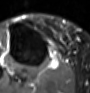
MRI of an extremity soft-tissue mass, one axial slice; slice 43 of 60 in the series (ordered by position); STIR; MR volume resampled by the dataset authors to the PET/CT grid (not the native acquisition matrix); 3.27 mm slice thickness; 90 × 93 image matrix, field of view 88 × 91 mm. Female patient. Case-level facts recorded for this patient, not image findings: histological type: undifferentiated – high grade; grade: high; site of the primary tumour: right thigh.
Annotated regions visible in this slice (expert contour drawn on MRI and transferred to this co-registered scan by the dataset authors):
- gross tumour volume (mass): bounding box <51,60,57,66> (left, top, right, bottom; pixels)